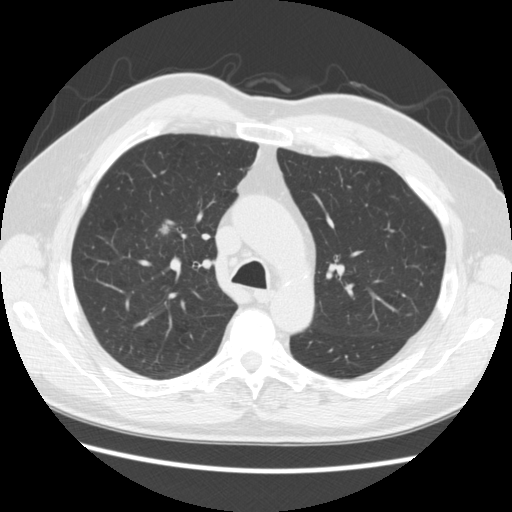
Low-dose screening chest CT, one axial slice; slice 179 of 259 in the series (ordered by position); lung window (W 1500 / L -600 HU); 2.5 mm slice thickness; 512 × 512 image matrix, field of view 360 × 360 mm.
Annotated regions visible in this slice (outlined manually by an expert reader):
- lesion 1 (tumor, upper lobe of right lung): bounding box [x1, y1, x2, y2] px = [159, 223, 169, 234]